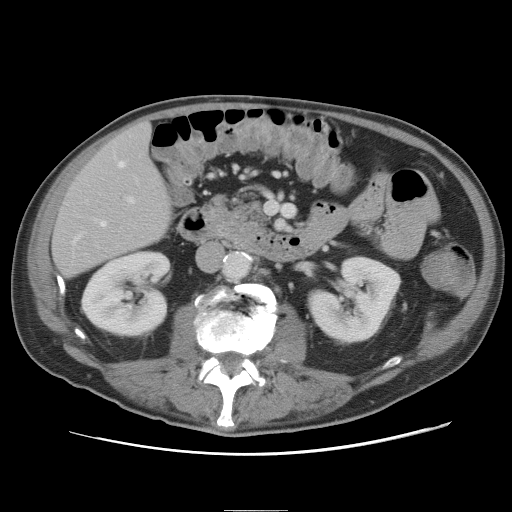
Contrast-enhanced abdominal CT, one axial slice; position 22 of 89 along the scan axis; 120 kVp; soft-tissue window (W 400 / L 40 HU); 5 mm slice thickness; 512 × 512 image matrix, field of view 375 × 375 mm. Male patient, age 69 years. From the clinical record (not read from this slice): diagnosis: colorectal cancer liver metastases, imaged before liver resection; multiple liver metastases: no; largest metastasis: 8.5 cm.
Outlined on this slice (expert manual segmentation):
- hepatic veins: box from (x=74, y=161) to (x=125, y=242) px
- liver: (x=52, y=123)–(x=172, y=276)
- planned liver remnant (the part of the liver to remain after resection): (x=54, y=123)–(x=171, y=276)
- portal vein (with intrahepatic branches): (x=127, y=196)–(x=135, y=203)